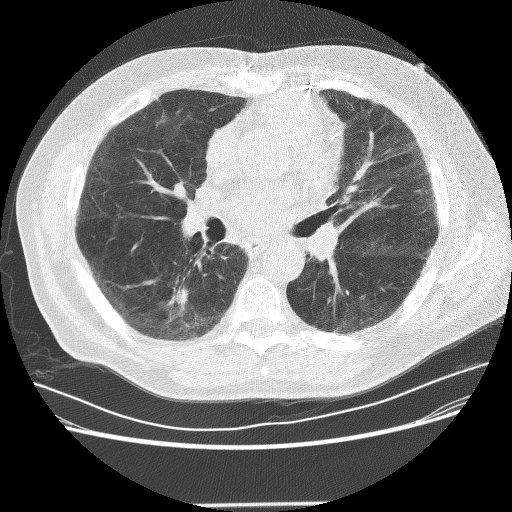
Axial slice from a low-dose chest CT screening exam, first (baseline) screen, lung window (W 1500 / L -600 HU), lung (sharp) reconstruction kernel (BONE). Male participant, aged 72 years at enrolment.
Expert reader's lesion annotation, box from (x=145, y=271) to (x=202, y=322) px. The screening reader recorded 2 non-calcified nodules or masses ≥4 mm on this exam (right lower lobe, left lower lobe); which of them this box marks is not recorded. Official screen result: positive, change unspecified: nodule(s) >= 4 mm or enlarging nodule(s), mass(es), or other non-specific abnormalities suspicious for lung cancer. Lung cancer was diagnosed 436 days after this screen: squamous cell carcinoma, NOS, right lower lobe, poorly differentiated (G3), stage IB (AJCC 6th edition), 42 mm at pathology.